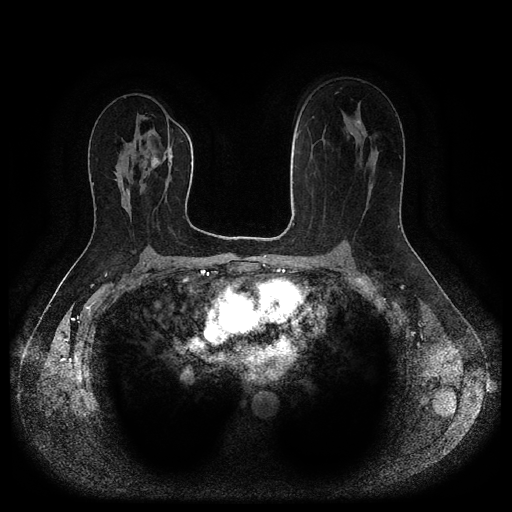
Breast MRI (dynamic contrast-enhanced, multi-phase), one axial slice; position 59 of 116 along the scan axis; dynamic contrast-enhanced series, time point 2 of 5 at this slice position (early post-contrast); 1.5 T; TE 2.6 ms, TR 5.3 ms; 512 × 512 image matrix. Patient: female, 53 years.
Structures marked on this image (semi-automatically segmented with operator editing):
- breast lesion (labelled benign in the annotation): bounding box [x1, y1, x2, y2] px = [152, 155, 158, 167]